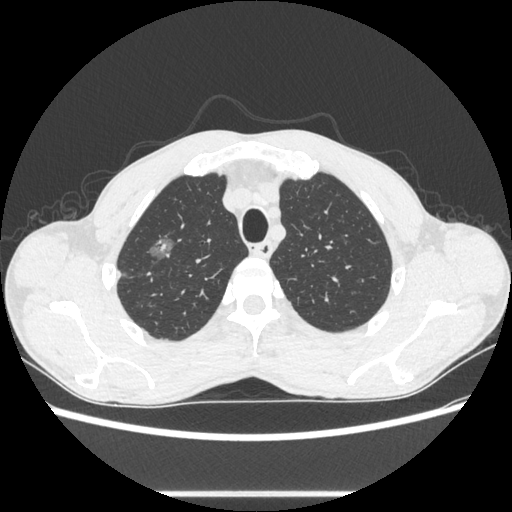
Chest CT, one axial slice; 100 kVp; lung window (W 1500 / L -600 HU); 0.62 mm slice thickness; 512 × 512 image matrix, field of view 357 × 357 mm. Male patient, age 54 years. Case-level facts recorded for this patient, not image findings: clinical TNM (as recorded): T1a N0 M0.
Outlined on this slice (bounding box drawn by a radiologist):
- lung tumour (recorded histology: adenocarcinoma): bounding box [x1, y1, x2, y2] px = [145, 230, 187, 268]